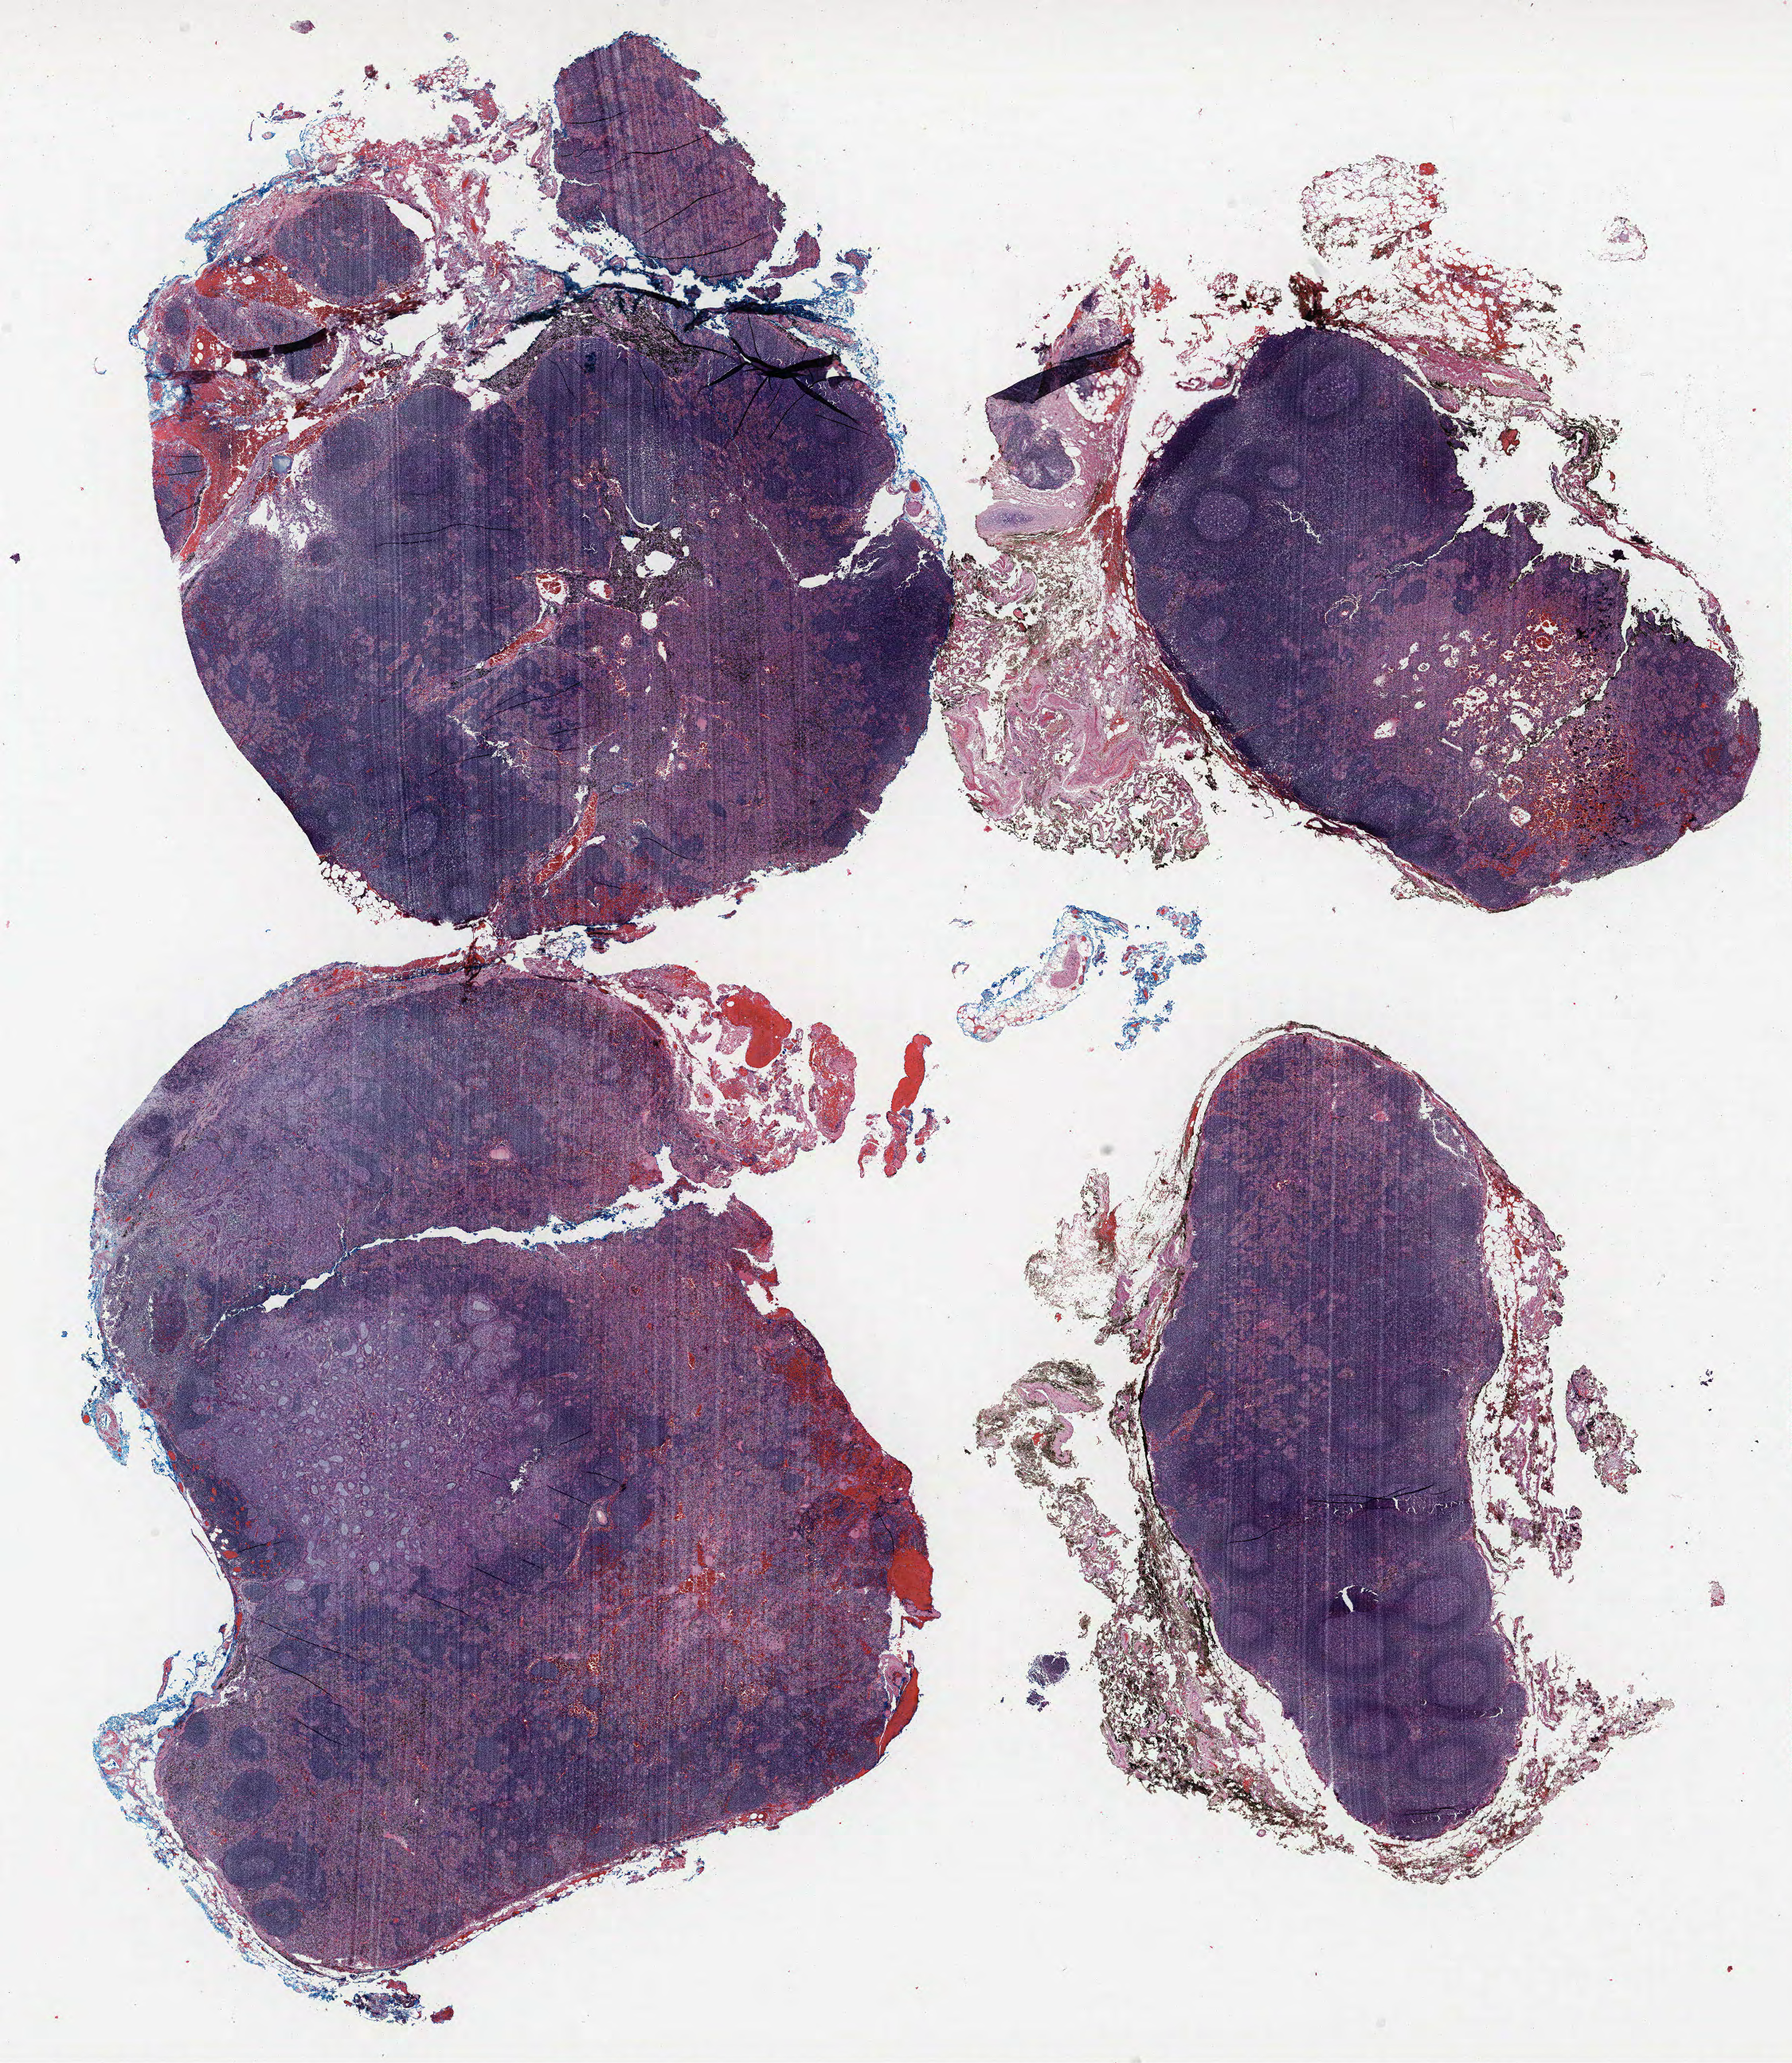
Whole-slide histology image, H&E, low-resolution overview of the scanned area, about 18.0 x 20.7 mm (acquisition: 40x scan). FFPE section. Lung. Female, age 71 at enrolment. Former smoker at enrolment. Grade: moderately differentiated (G2).
Tumour size (pathology): 12 mm. Primary tumour location (clinical record): left upper lobe. ICD-O-3 topography: upper lobe of lung (C34.1). Participant's lung-cancer diagnosis: Adenocarcinoma, NOS (ICD-O-3 8140/3). Stage (AJCC 6th edition): IIA.